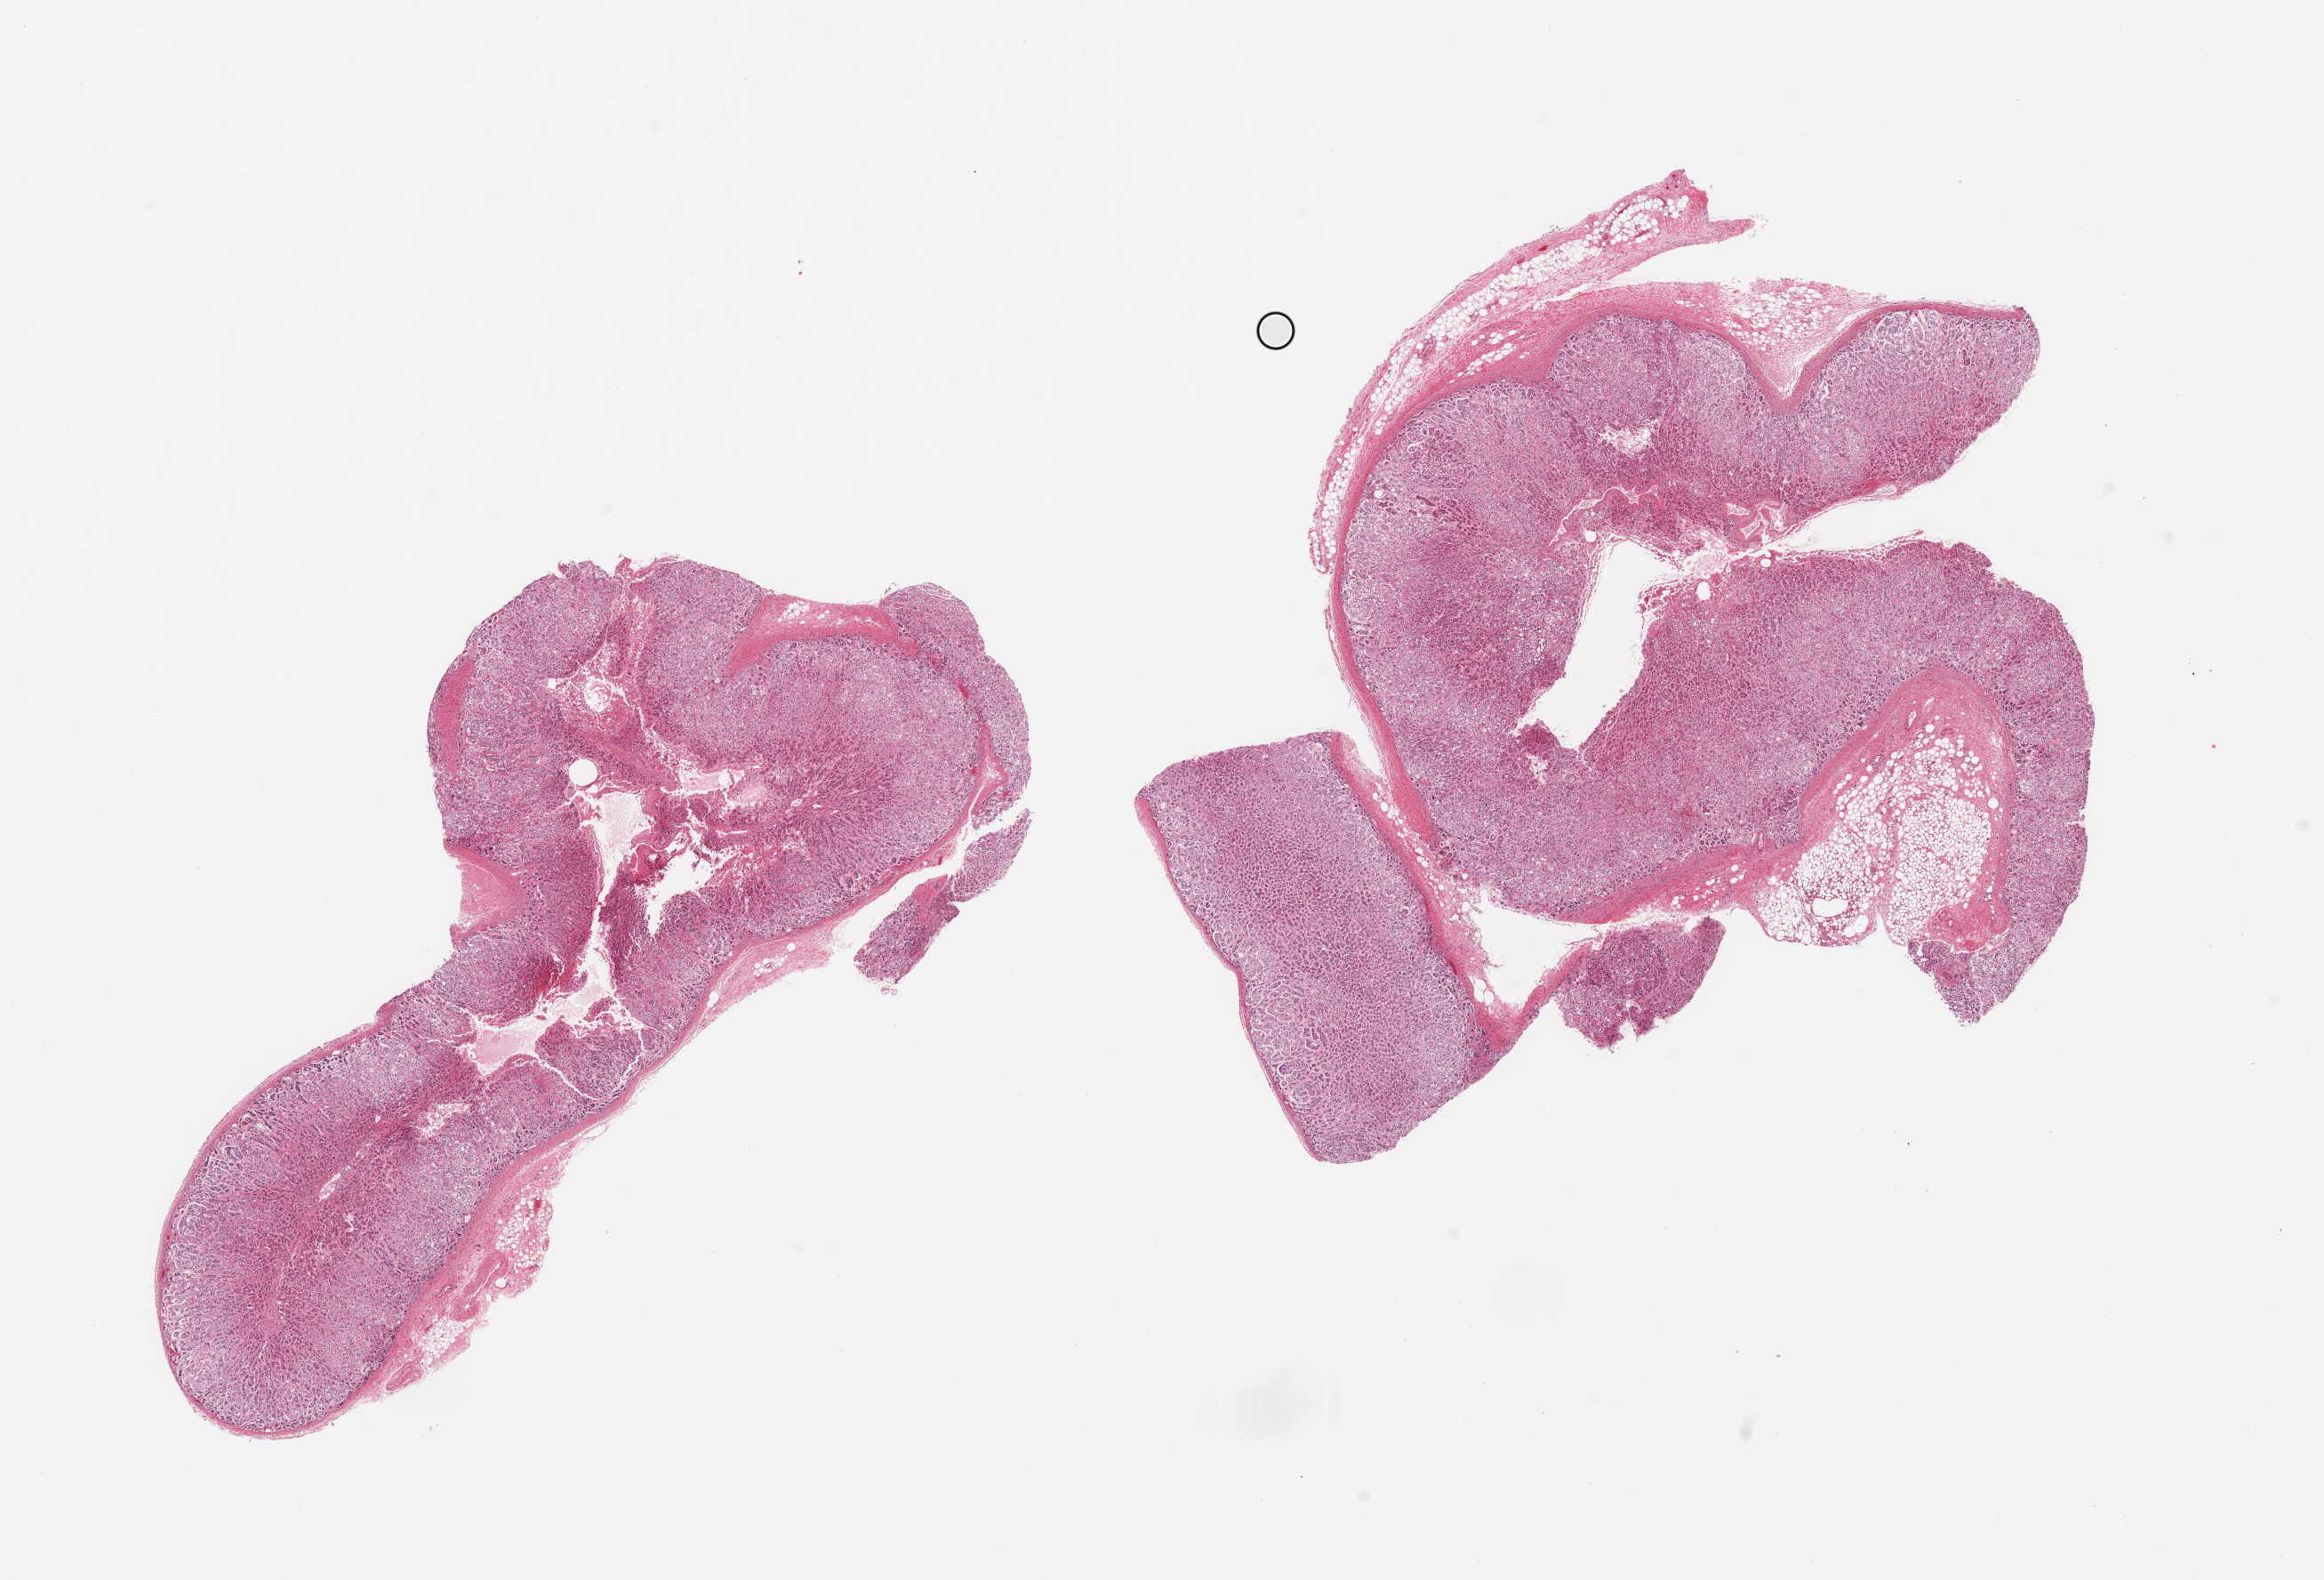
Digitized haematoxylin and eosin-stained section — whole scanned area (about 20.7 x 14.1 mm) shown as a low-resolution overview; PAXgene-fixed paraffin-embedded (PFPE) section; sampled site (target tissue): adrenal gland; donor tissue sample. Donor: female.
Pathologist's review note for this sample: 2 pieces, ~10% adherent fat; All cortex, mild-moderate autolysis, some areas approach score '2'.